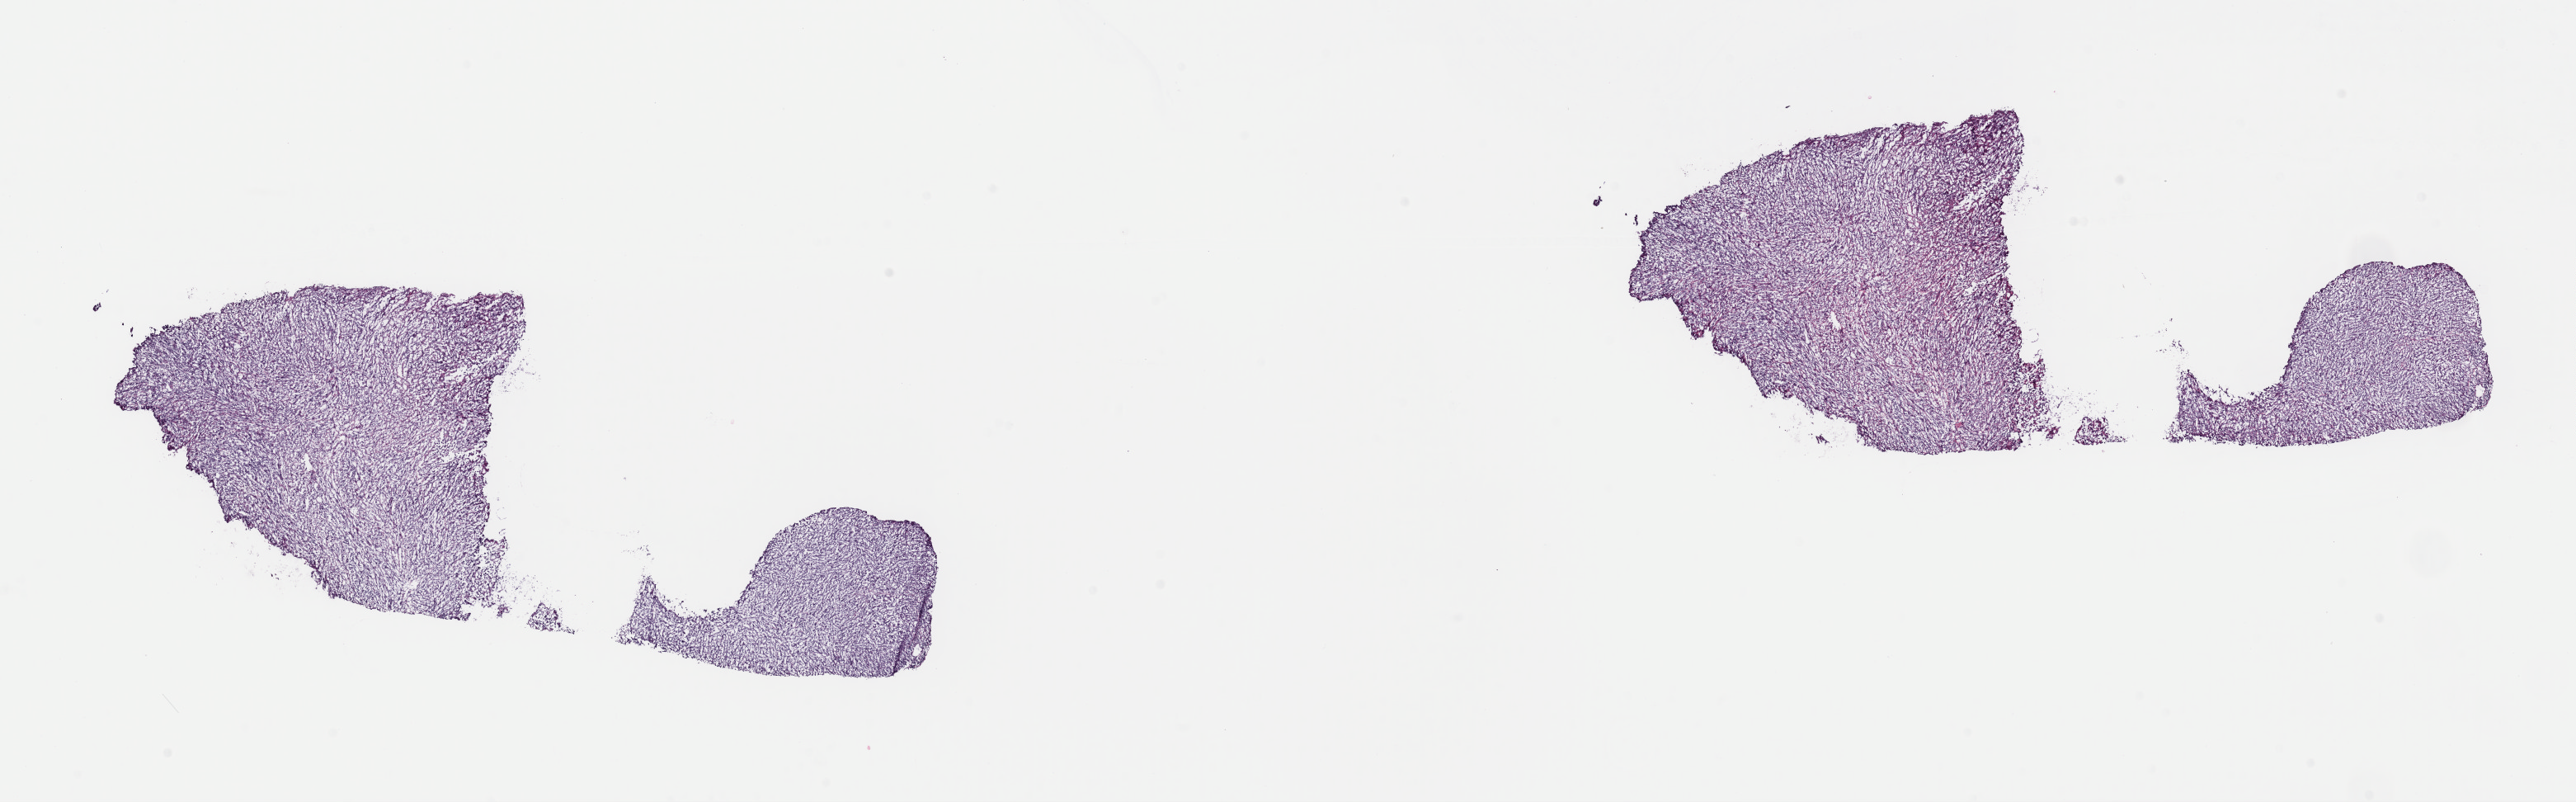
Digitized H&E tissue section (whole slide) — whole scanned area (about 24.7 x 7.7 mm, slide scanned at 40x) shown as a low-resolution overview, frozen section, sample: primary tumour, liver. Patient: male, age at initial diagnosis 45 years. Histologic grade: G3 (poorly differentiated). Pathologist review of this section (percent, as recorded): tumour cells 70%, tumour nuclei 70%, normal cells 0%, stromal cells 30%, necrosis 0%. Infiltration values recorded for this section: lymphocyte infiltration 7%, monocyte infiltration 1%, neutrophil infiltration 2%.
Pathologic diagnosis: Hepatocellular carcinoma, spindle cell variant. AJCC pathologic stage: IIIA (7th edition).